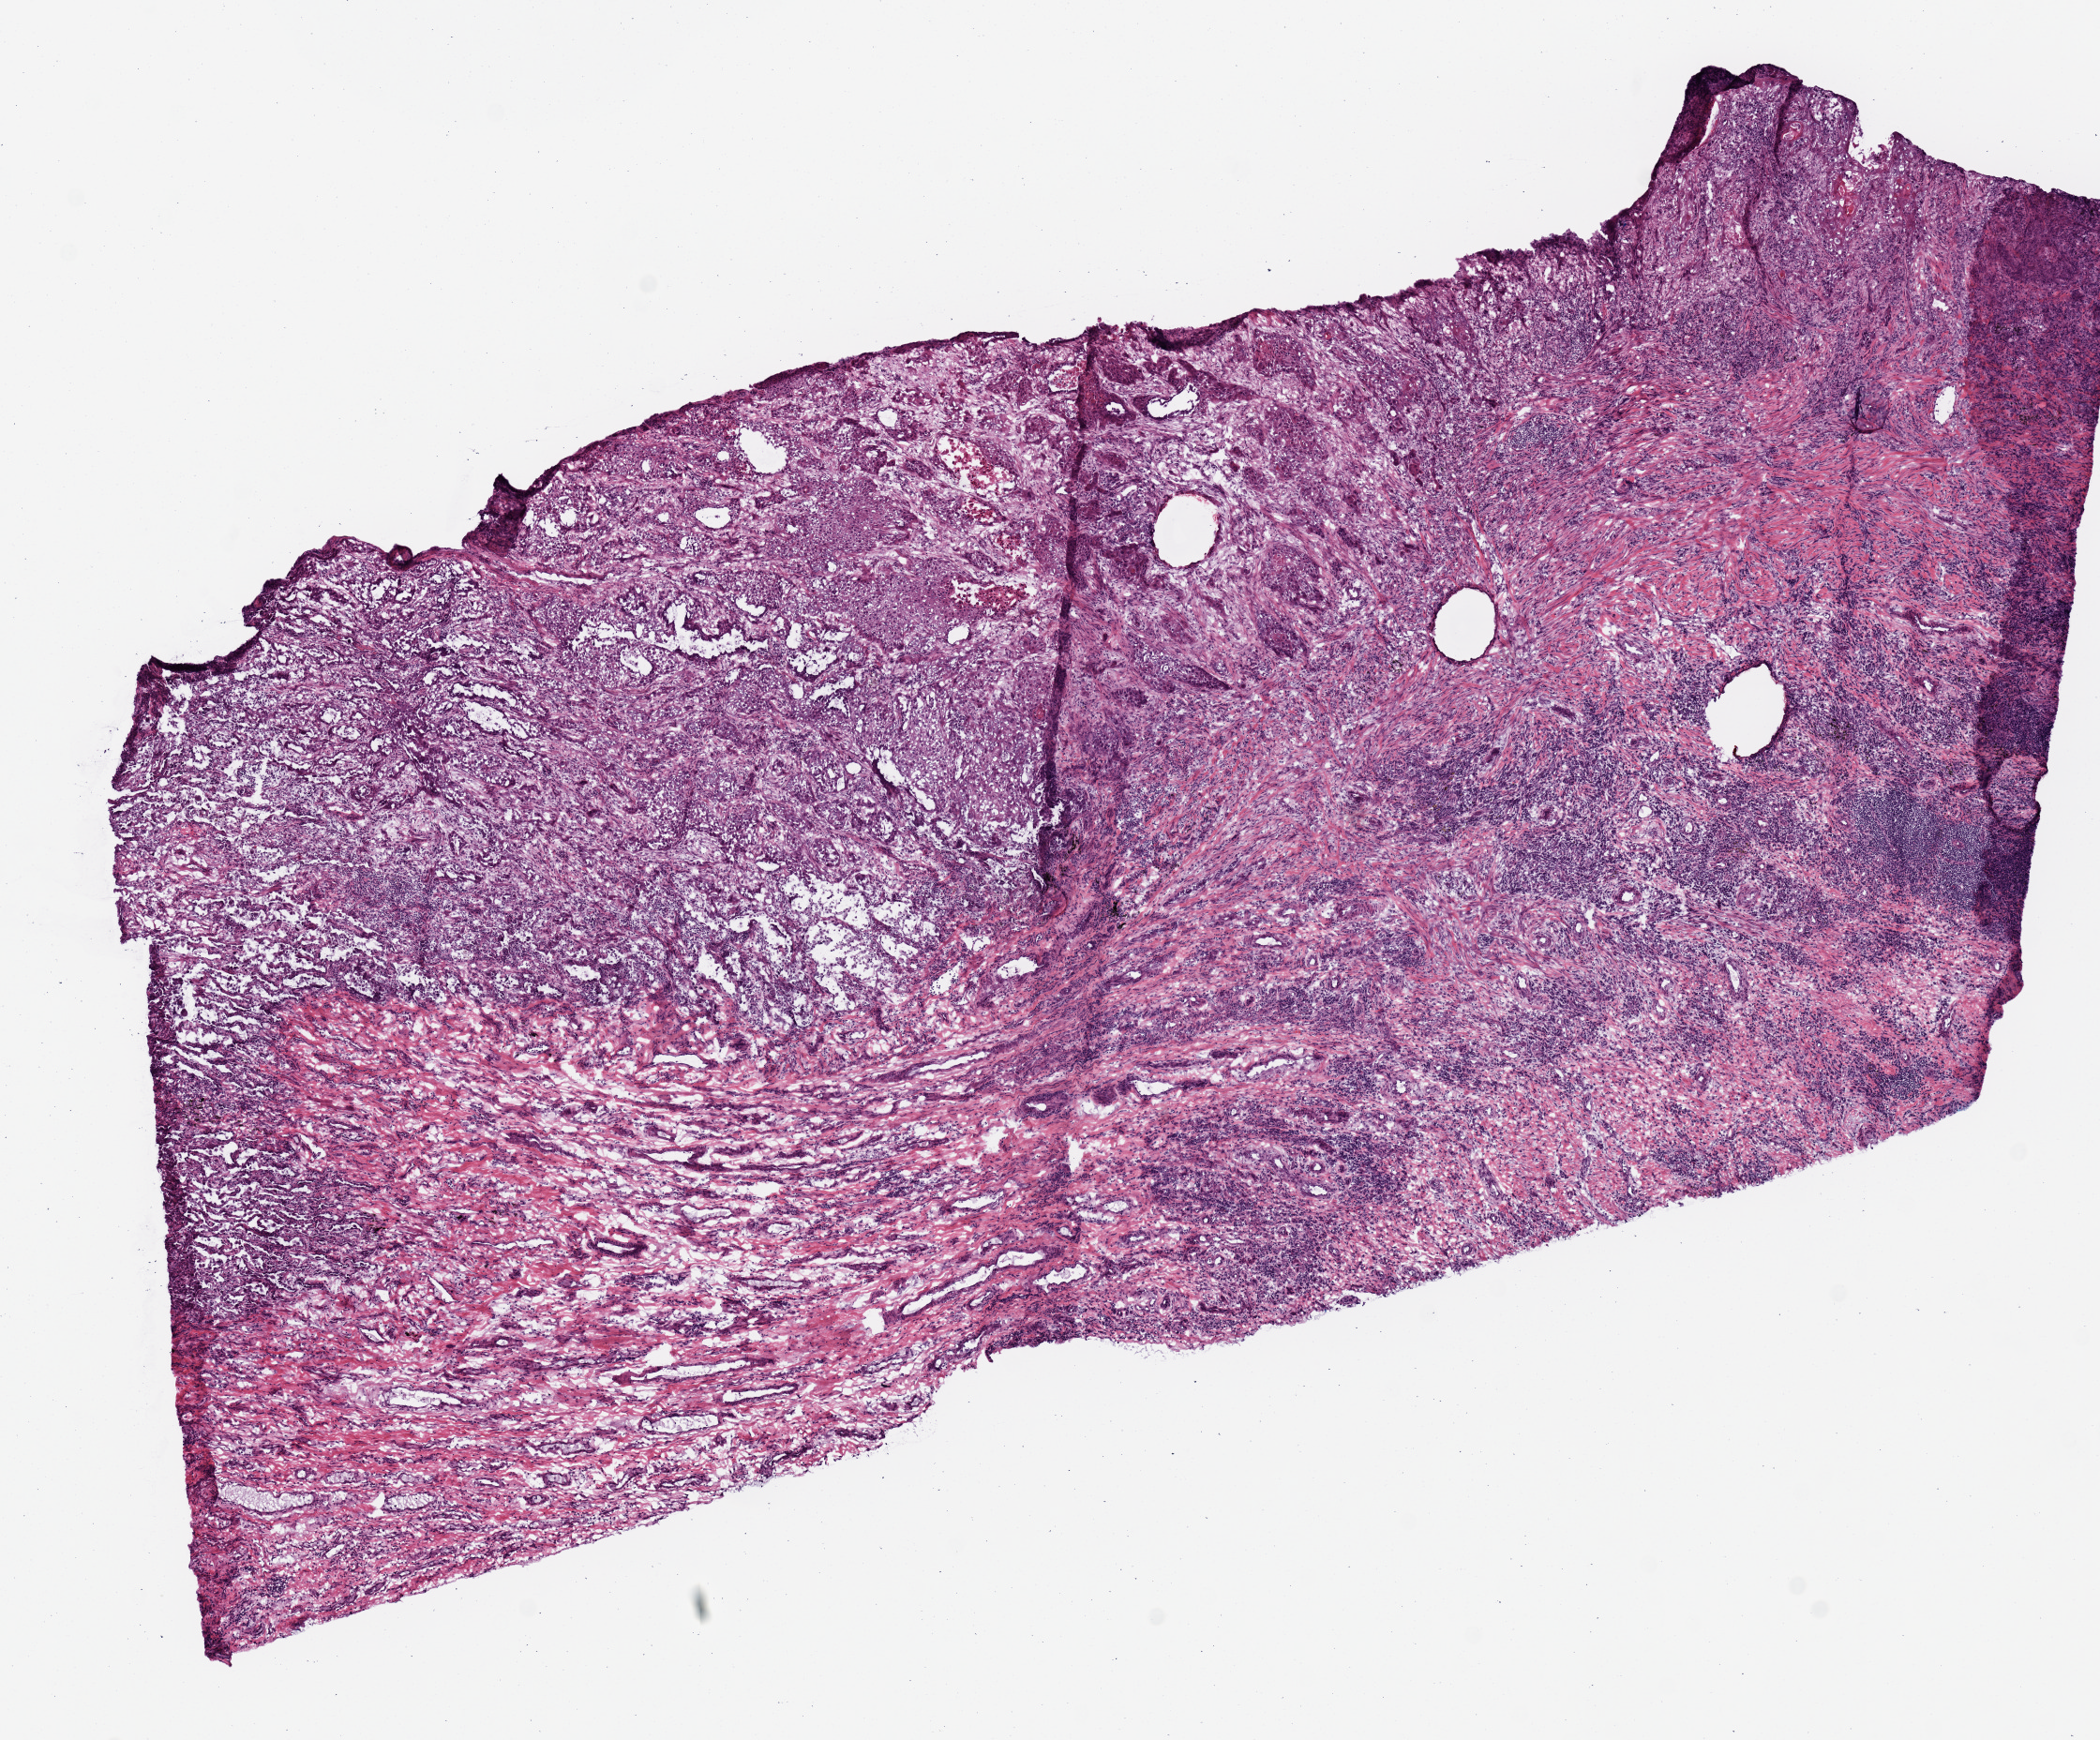
Digitized Hematoxylin and eosin (H&E) stained tissue section (whole slide), low-resolution overview of the scanned area, about 8.9 x 7.3 mm (slide scanned at 20x), frozen section from the top of the tissue portion, primary tumour sample from the lung. Male, age 68 years at initial diagnosis. Slide review estimates, as recorded: tumour cells 100%, tumour nuclei 80%.
Diagnosis: Squamous cell carcinoma, NOS.